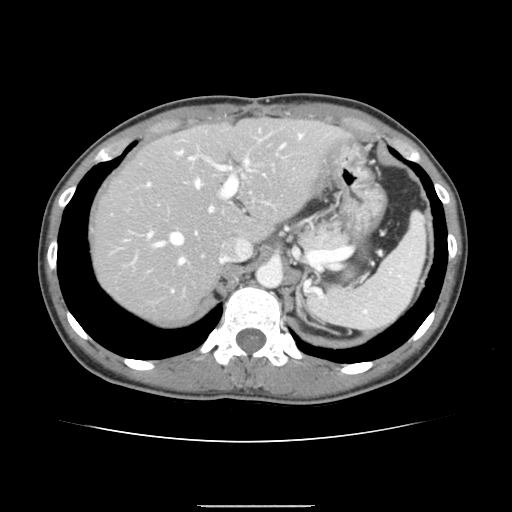
Contrast-enhanced abdominal CT, one axial slice; position 108 of 150 along the scan axis; 120 kVp; intravenous contrast given; soft-tissue window (W 400 / L 40 HU); 2.5 mm slice thickness; 512 × 512 image matrix, field of view 324 × 324 mm. Female patient, age 32 years. From the clinical record (not read from this slice): diagnosis: colorectal cancer liver metastases, imaged before liver resection; multiple liver metastases: yes; largest metastasis: 0.7 cm; disease in both lobes: no.
Annotated regions visible in this slice (expert manual segmentation):
- hepatic veins: box from (x=153, y=159) to (x=249, y=265) px
- liver: (x=93, y=120)–(x=342, y=322)
- planned liver remnant (the part of the liver to remain after resection): (x=92, y=120)–(x=342, y=279)
- portal vein (with intrahepatic branches): (x=148, y=134)–(x=303, y=291)